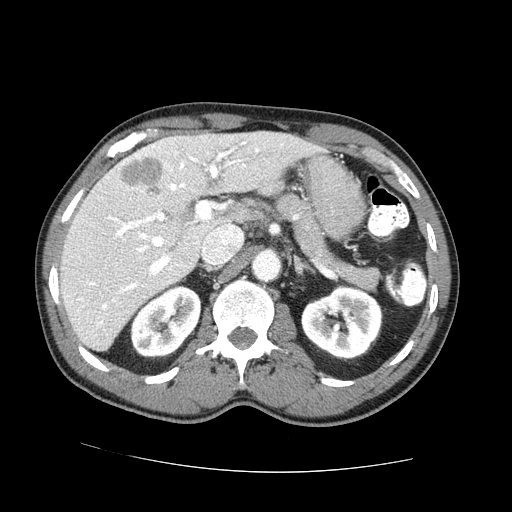
Contrast-enhanced abdominal CT (liver protocol), one axial slice; slice 43 of 73 in the series (ordered by position); 100 kVp; one of 2 acquisitions stored at this slice position; soft-tissue window (W 400 / L 40 HU); 2.5 mm slice thickness; 512 × 512 image matrix. Case-level facts recorded for this patient, not image findings: diagnosis: hepatocellular carcinoma (patient treated with transarterial chemoembolisation; whether this scan precedes or follows treatment is not stated here); TNM stage (as recorded): Stage-IVA; Child-Pugh class: A.
Structures marked on this image (semi-automatic segmentation, software-assisted and operator-edited):
- liver parenchyma outside the tumour (the mass and vessels are separate outlines, so this box may not span the whole liver): box from (x=60, y=132) to (x=316, y=350) px
- mass: (x=121, y=158)–(x=161, y=194)
- liver vessels: (x=79, y=142)–(x=259, y=325)